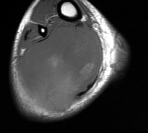
MRI of an extremity soft-tissue mass, one axial slice; position 37 of 76 along the scan axis; MR volume resampled by the dataset authors to the PET/CT grid (not the native acquisition matrix); 3.27 mm slice thickness; 148 × 133 image matrix. Male patient. From the clinical record (not read from this slice): histological type: liposarcoma - round cell; grade: high; site of the primary tumour: right calf.
Structures marked on this image (expert contour drawn on MRI and transferred to this co-registered scan by the dataset authors):
- gross tumour volume (mass): box from (x=20, y=26) to (x=103, y=113) px